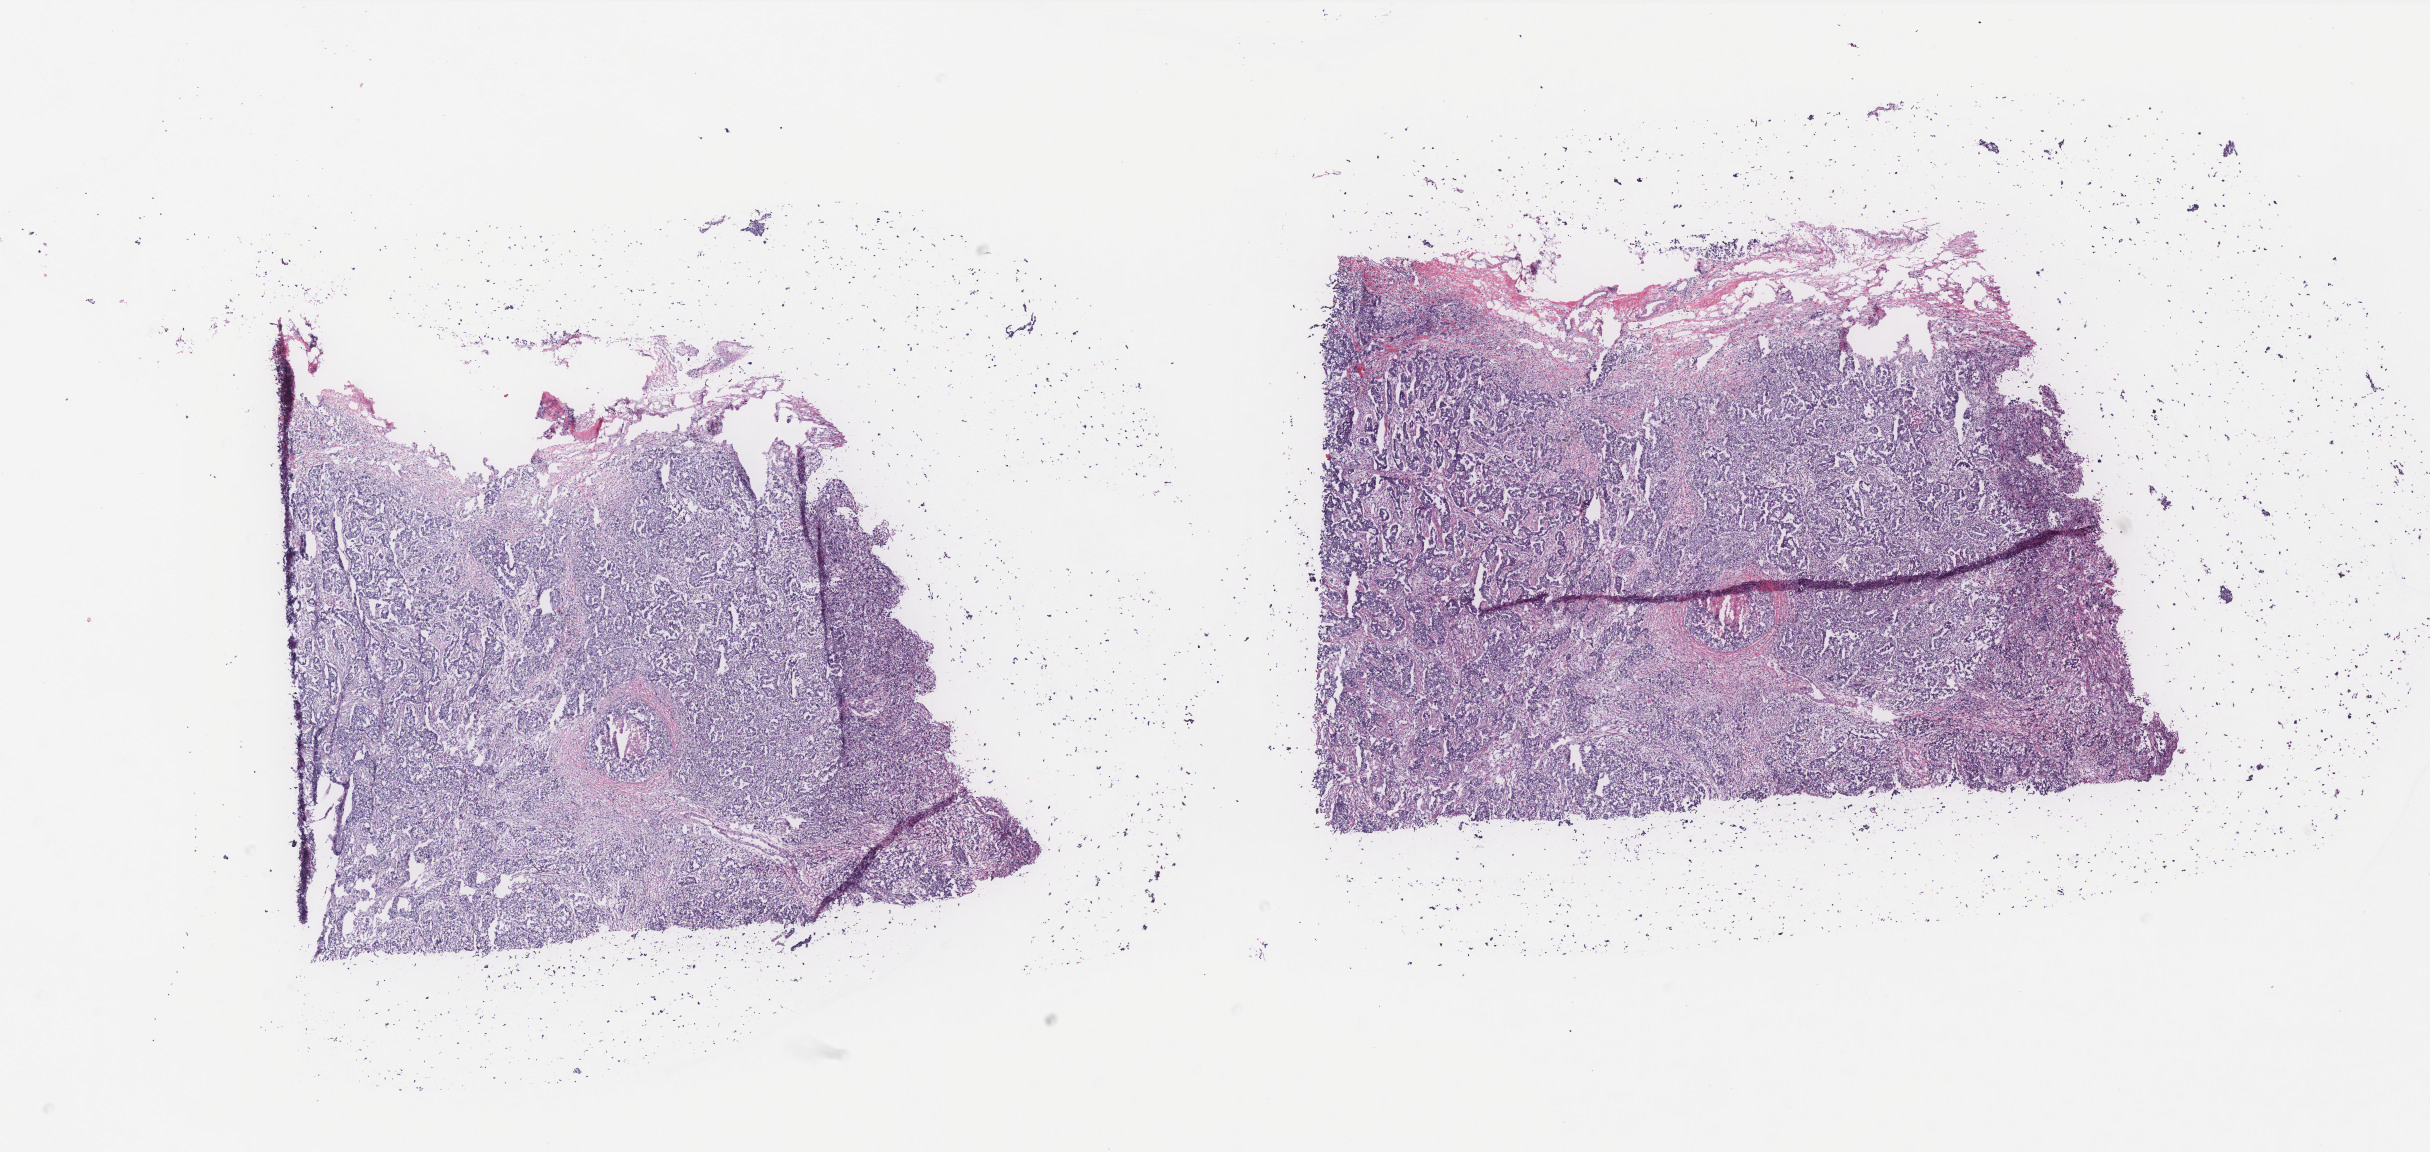
Hematoxylin and eosin (H&E) stained whole-slide image — a low-resolution overview of the entire scanned area, about 19.5 x 9.2 mm. Frozen section from the top of the tissue portion. Primary tumour sample from the breast. Female, age 43 years at initial diagnosis. Composition of this section per pathologist review: tumour cells 85%, tumour nuclei 90%.
Pathologic diagnosis: Infiltrating duct carcinoma, NOS.